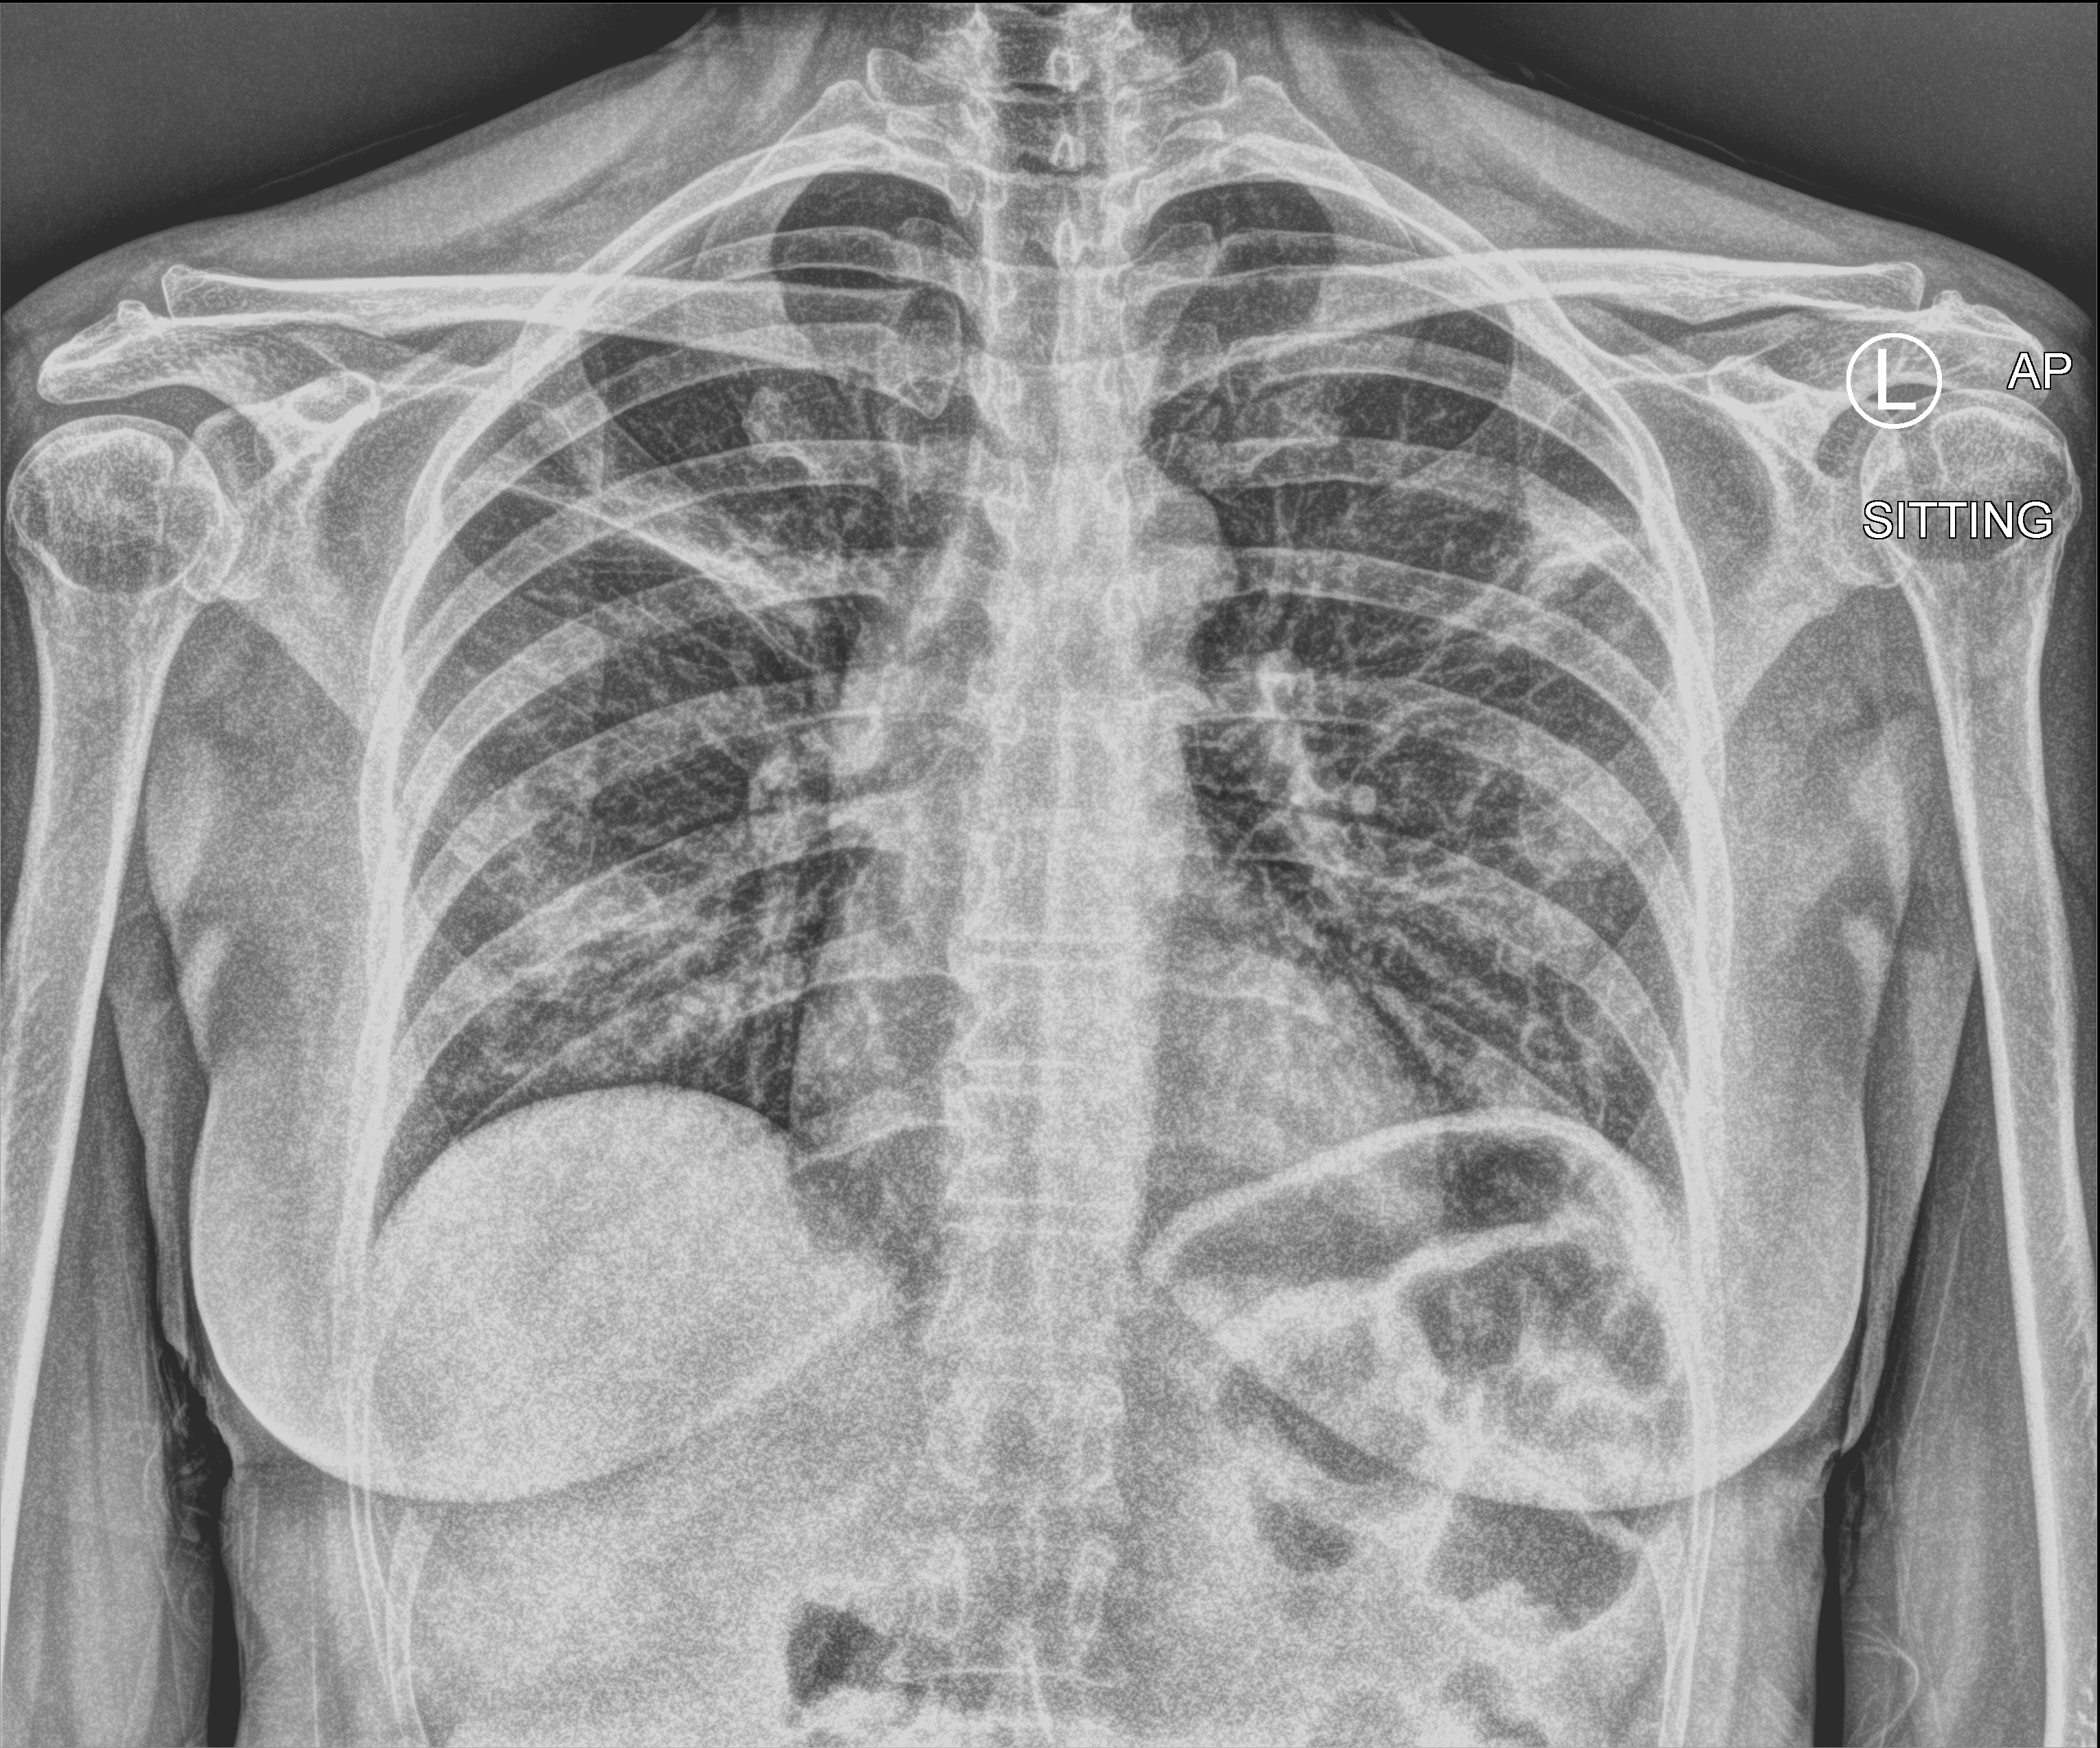
Bedside chest radiograph (computed radiography), anteroposterior (AP) projection. Patient hospitalised with COVID-19; female, aged 18–59 years.
Admission-level facts for this patient (not findings on this image; timing relative to this image not recorded): admitted to intensive care during this hospital stay: no; hypertension (admission record): no.